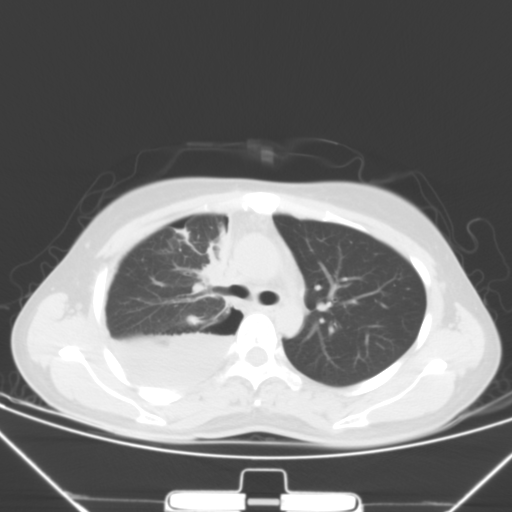
Chest CT, one axial slice. Slice 38 of 57 in the series (ordered by position). Lung window (W 1500 / L -600 HU). 5 mm slice thickness. 512 × 512 image matrix, field of view 343 × 343 mm. Patient: female, 28 years. From the clinical record (not read from this slice): clinical TNM (as recorded): T2 N0 M1a.
Annotated regions visible in this slice (rectangle marked by the reading radiologist):
- lung tumour (recorded histology: adenocarcinoma): bounding box [x1, y1, x2, y2] px = [197, 227, 230, 300]